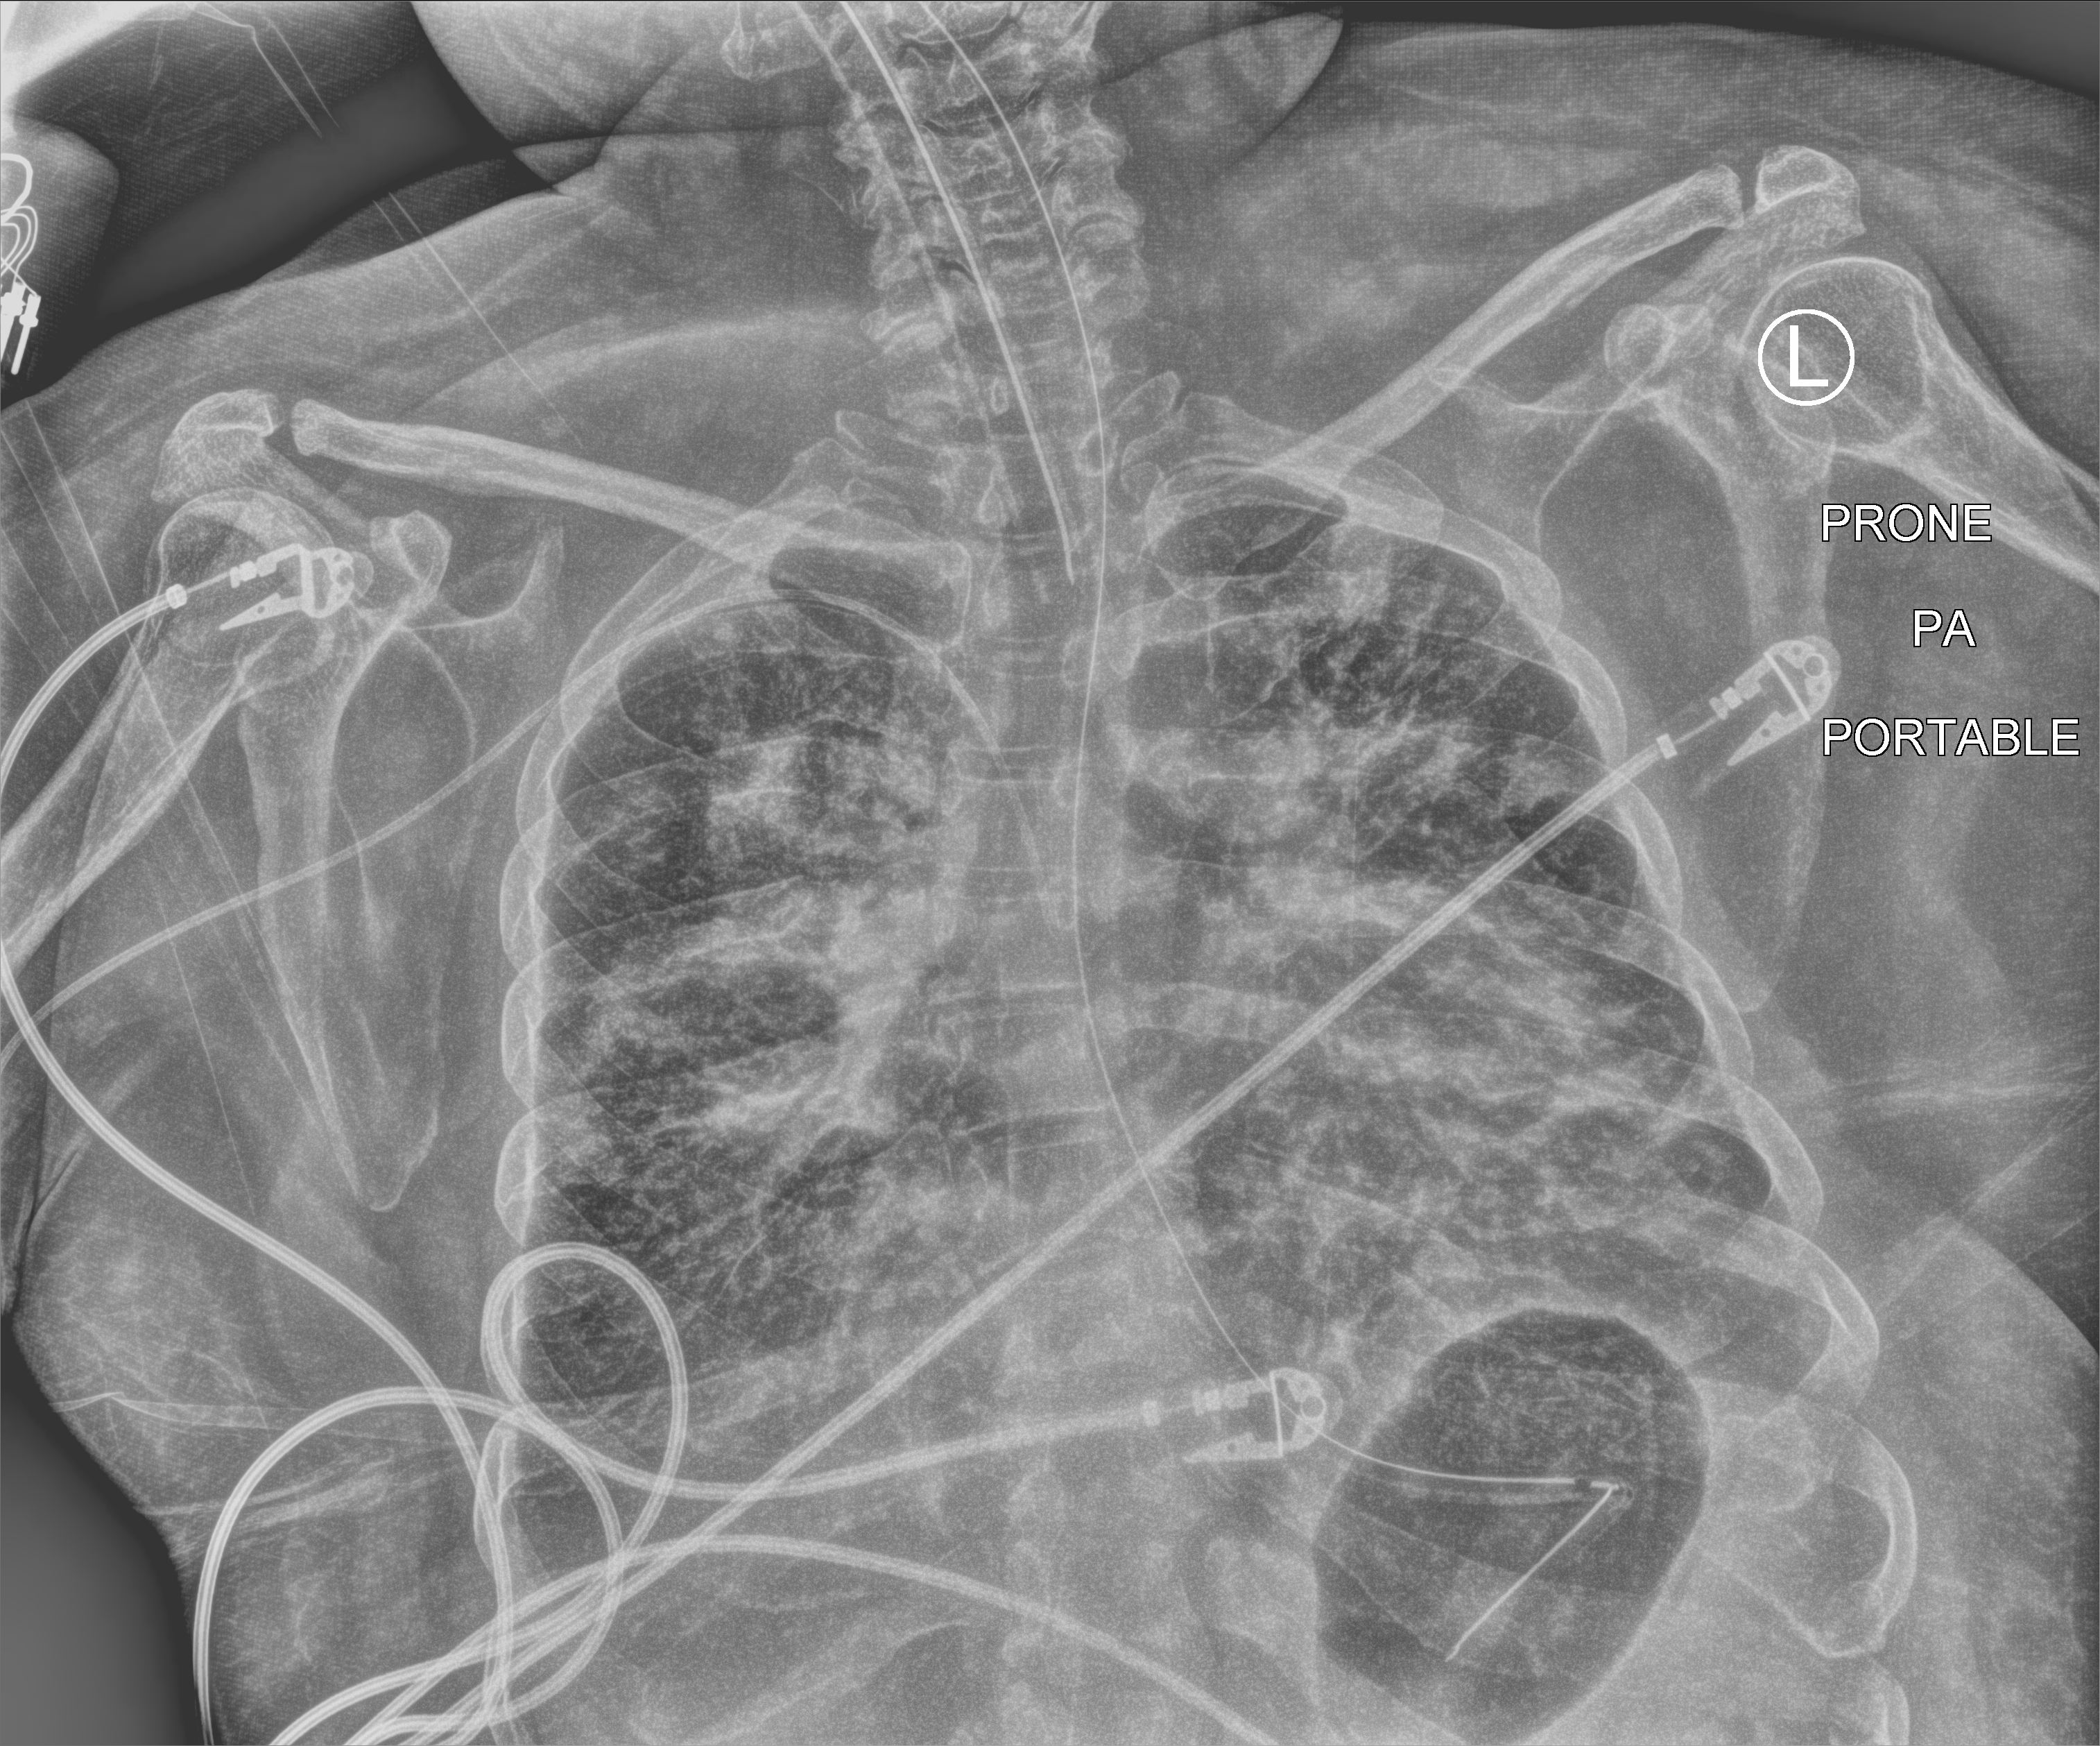
Bedside chest radiograph (computed radiography). Adult patient hospitalised with COVID-19, age 18–59 years.
Admission-level facts for this patient (not findings on this image; timing relative to this image not recorded):
- mechanically ventilated during this hospital stay: yes